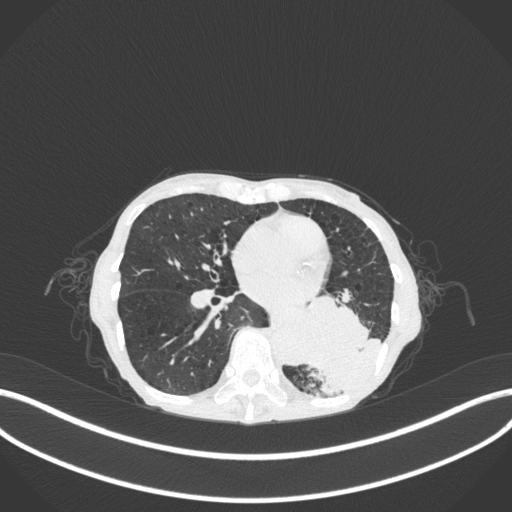
Chest CT, one axial slice. Slice 120 of 347 in the series (ordered by position). Reconstruction kernel B31f. 120 kVp. Lung window (W 1500 / L -600 HU). 1 mm slice thickness. 512 × 512 image matrix, field of view 400 × 400 mm. Patient: female, 70 years. From the clinical record (not read from this slice): clinical TNM (as recorded): T3 N0 M0.
Outlined on this slice (rectangle marked by the reading radiologist):
- lung tumour (recorded histology: small cell carcinoma): box from (x=305, y=292) to (x=388, y=400) px